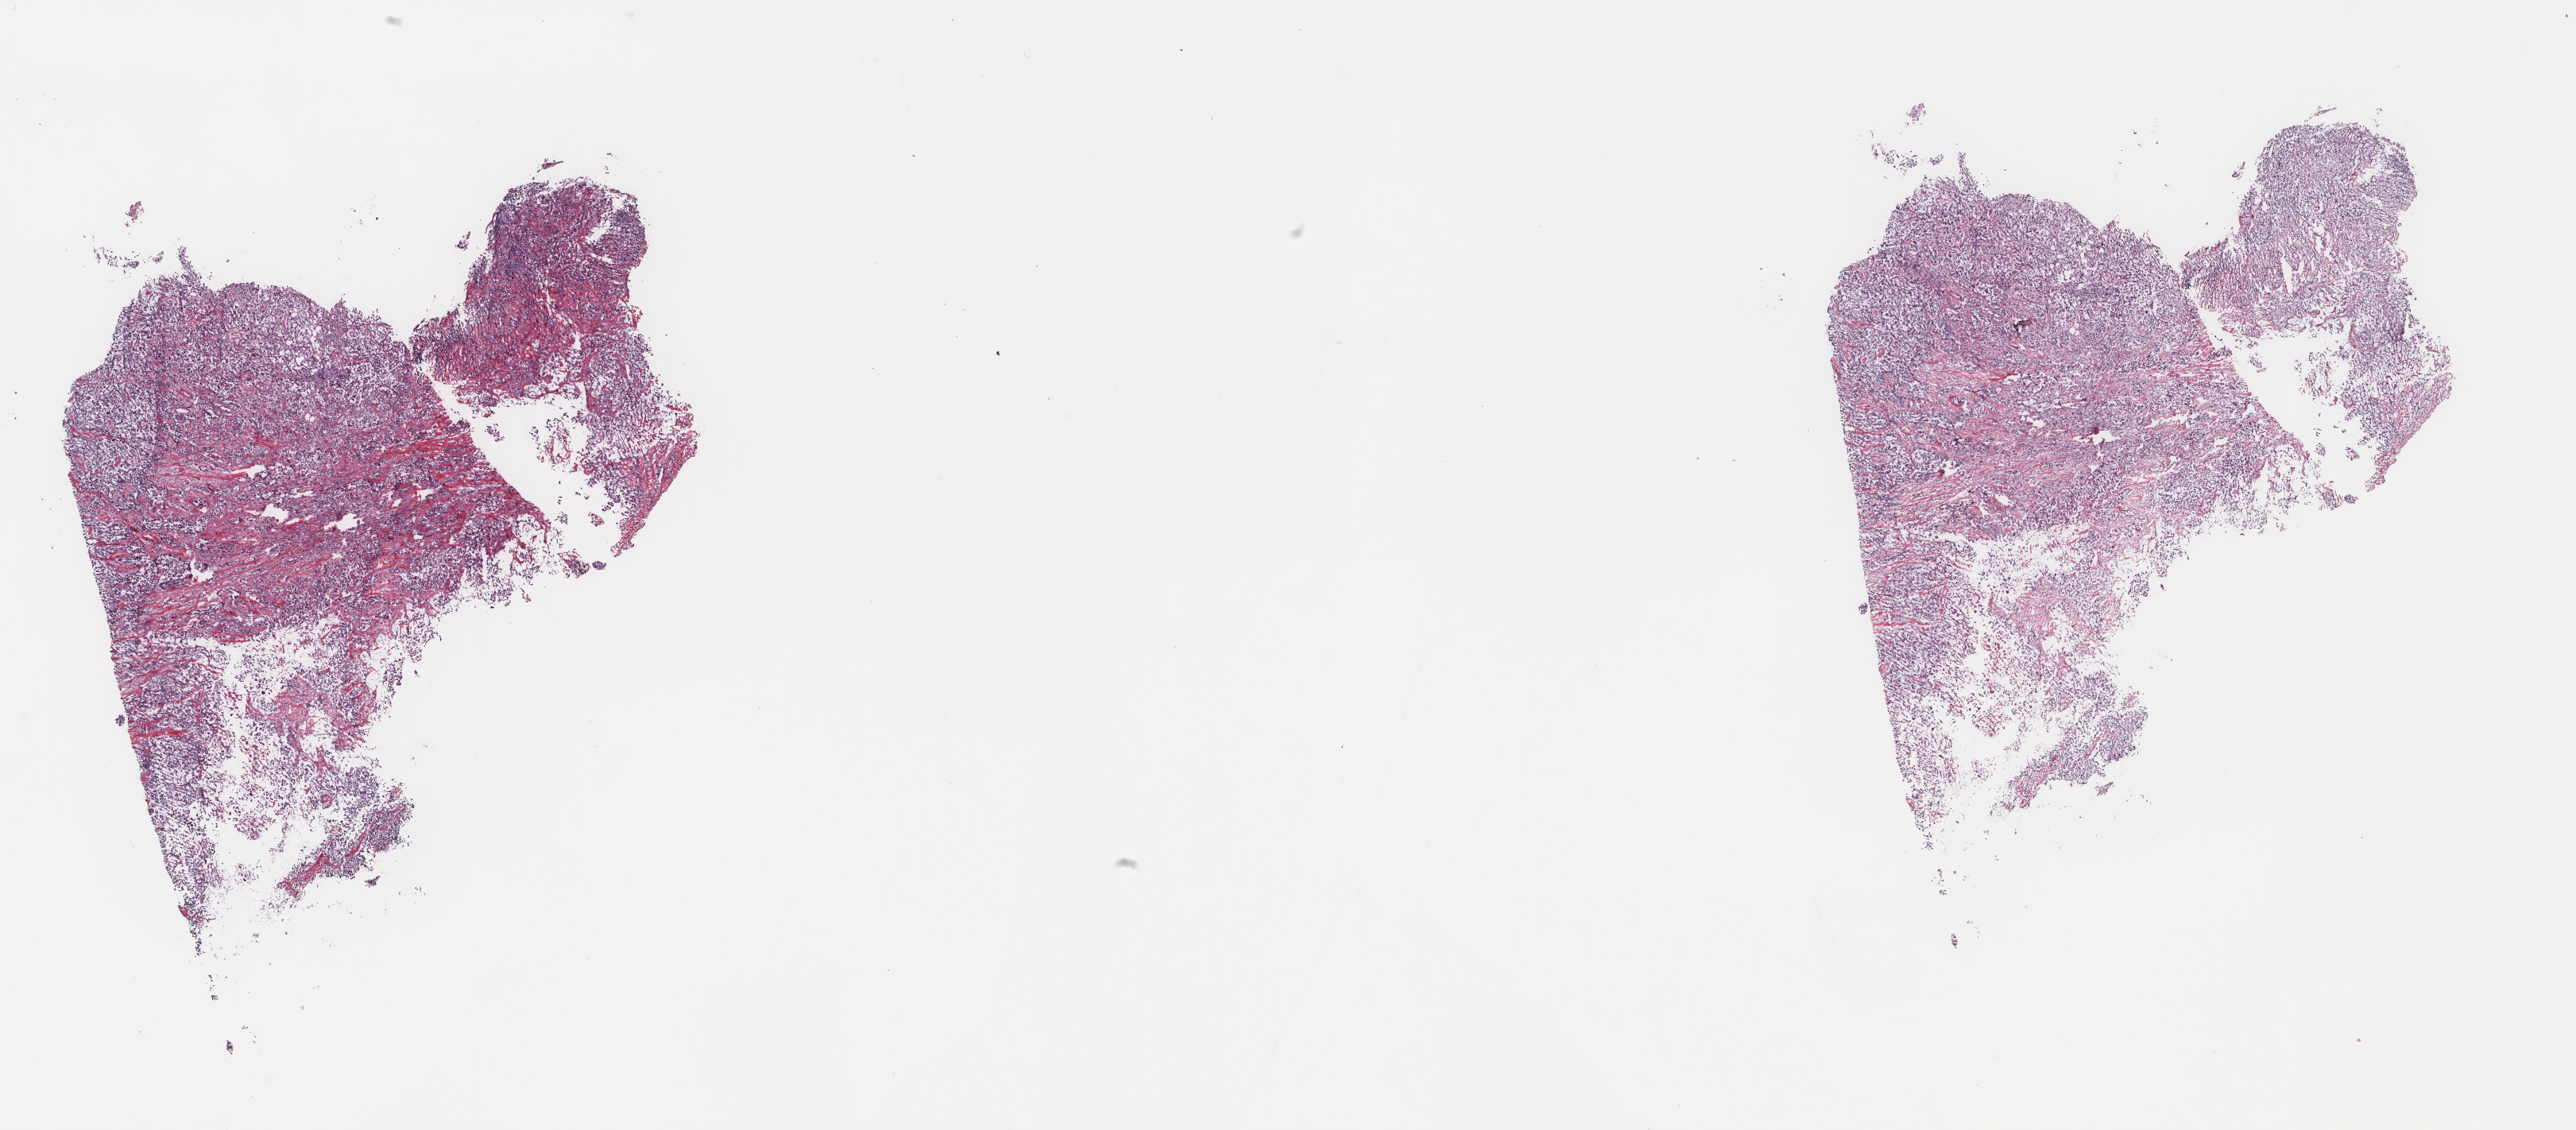
Whole-slide histology image, H&E, whole scanned area (about 25.7 x 11.3 mm, slide scanned at 40x) shown as a low-resolution overview. Frozen section. Mesothelium, primary tumour sample. Female, age 68 years at initial diagnosis. Pathologist review of this section (percent, as recorded): tumour cells 100%, tumour nuclei 95%, normal cells 0%, stromal cells 0%, necrosis 0%. Infiltration values recorded for this section: lymphocyte infiltration 0%, monocyte infiltration 0%, neutrophil infiltration 0%.
TNM: T3 N0 M0. Histologic diagnosis: Epithelioid mesothelioma, malignant (pleura, NOS). AJCC pathologic stage: III (7th edition).